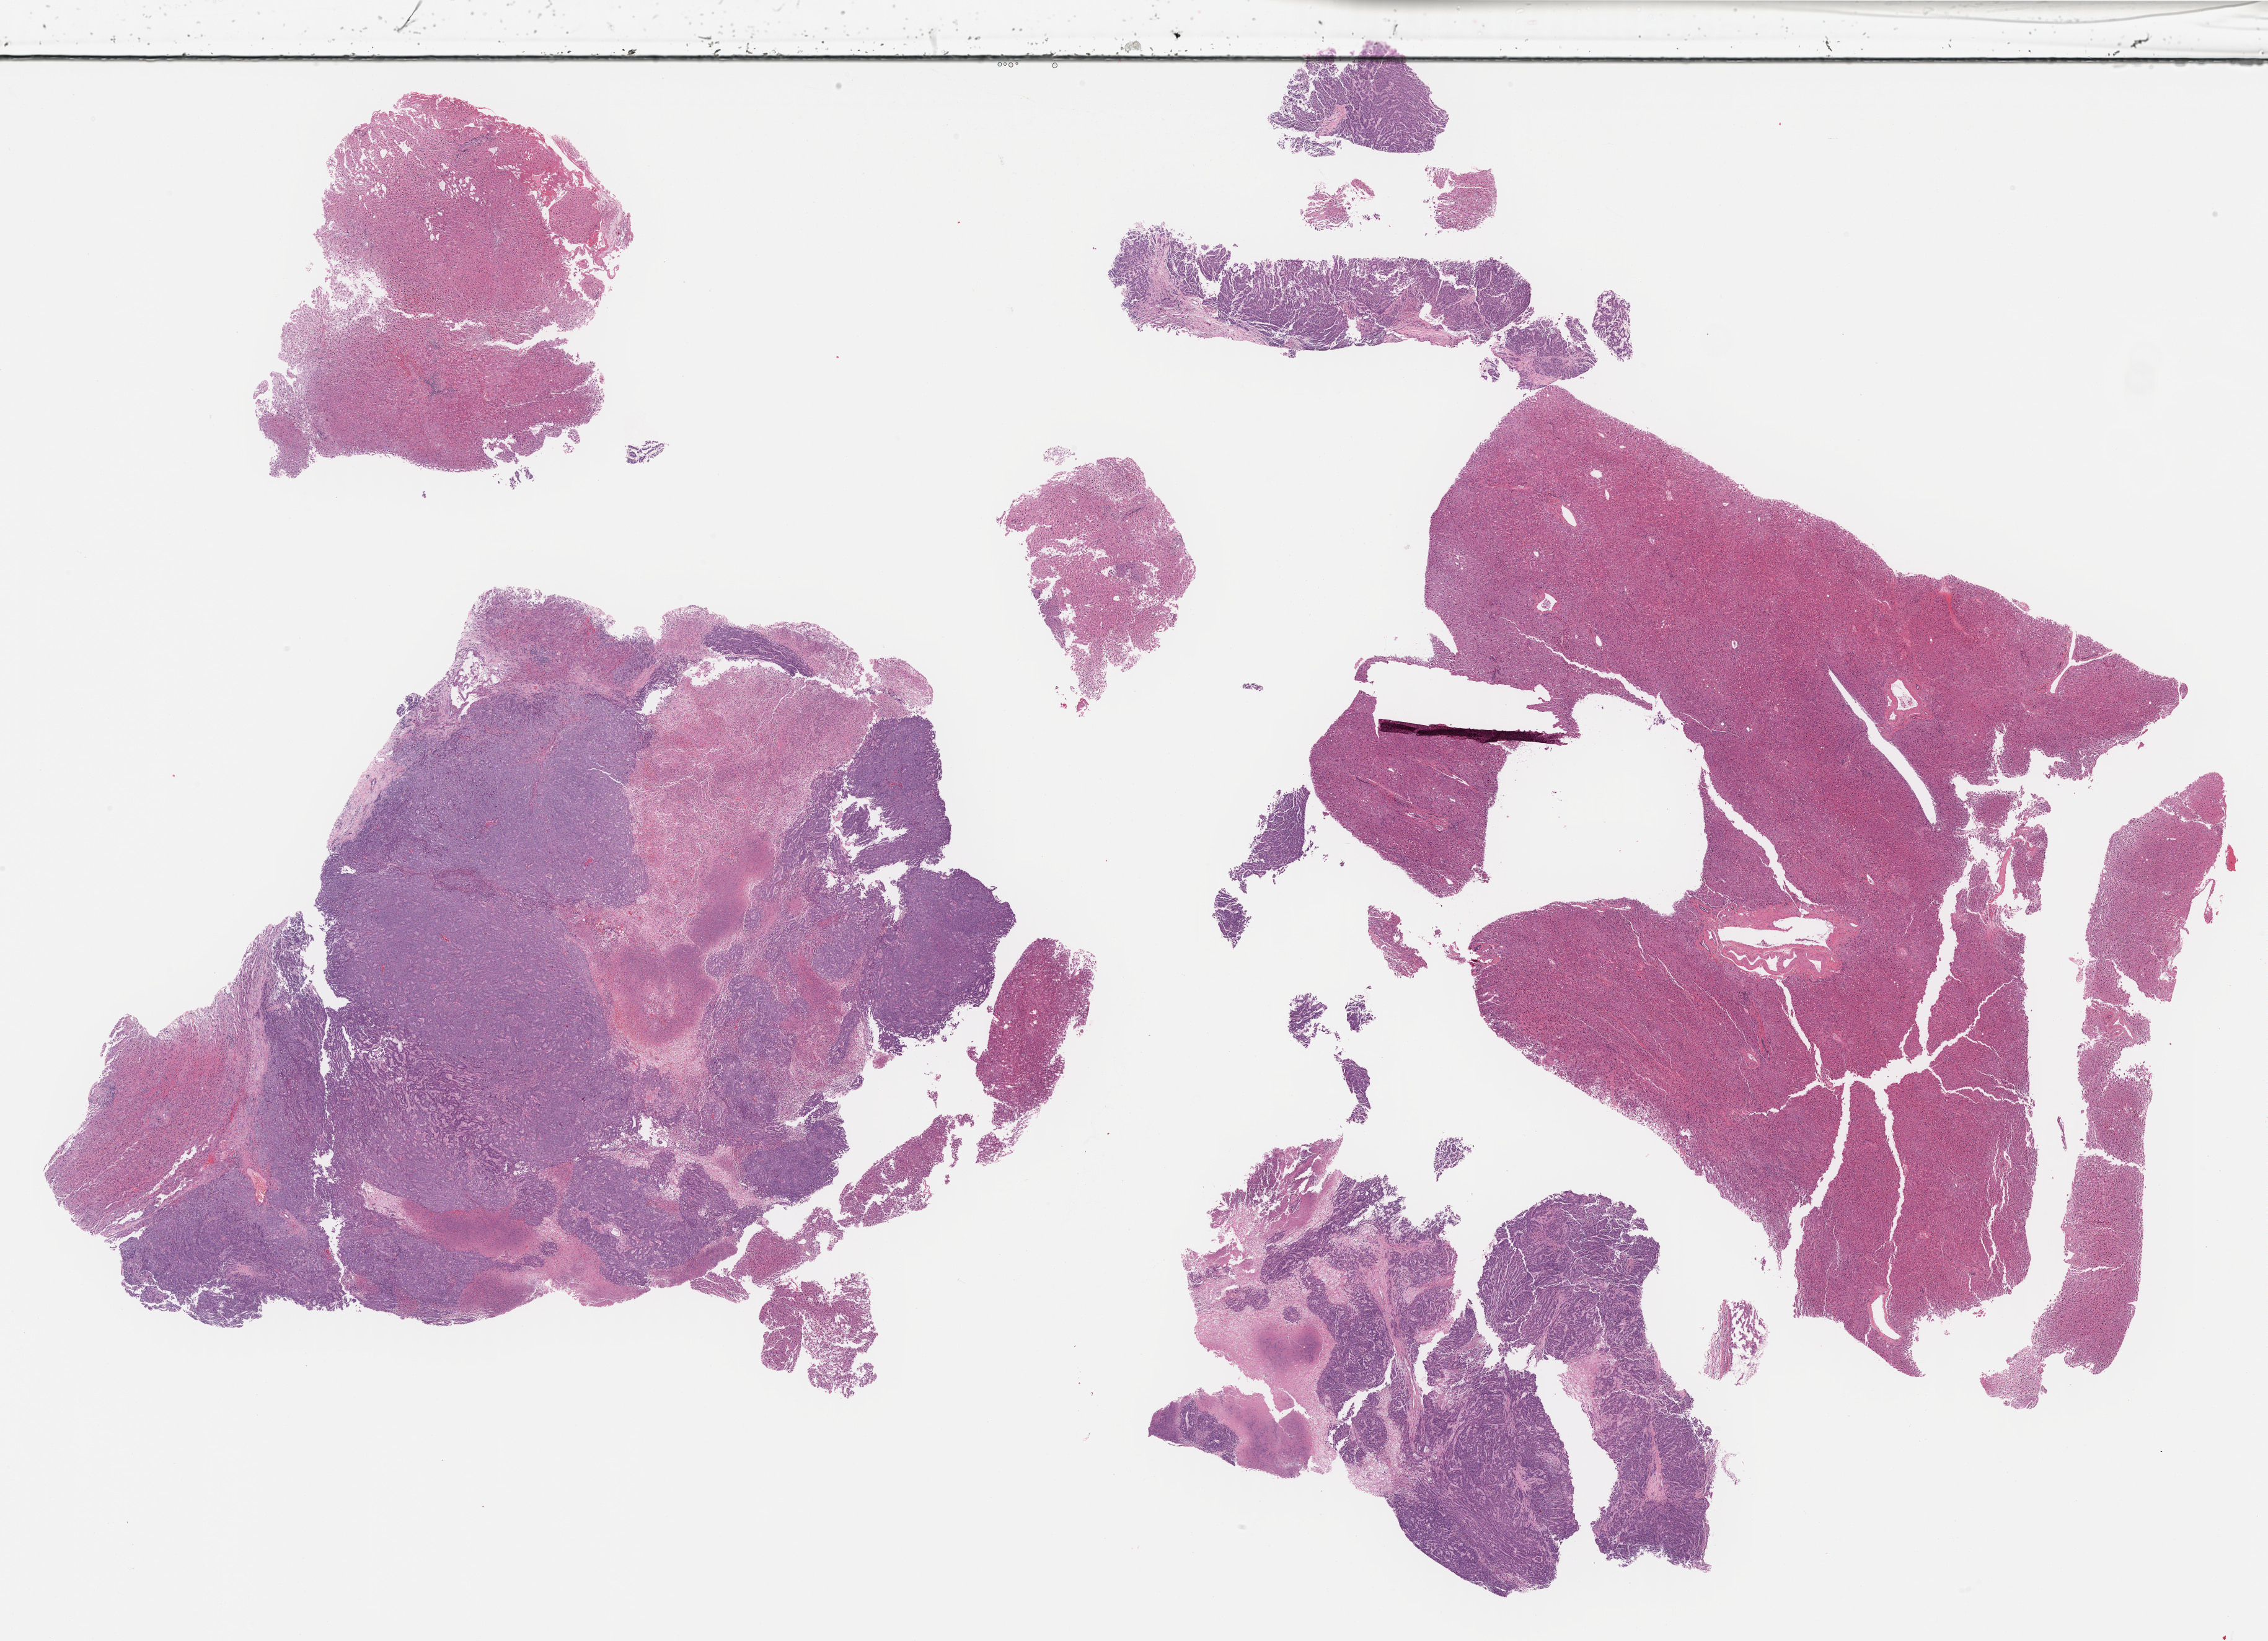
H&E whole-slide image — whole scanned area (about 29.6 x 21.4 mm) shown as a low-resolution overview, formalin-fixed paraffin-embedded (FFPE) diagnostic section, liver, primary tumour sample. Patient: female, age at initial diagnosis 81 years. Histologic grade: G4 (undifferentiated).
• AJCC pathologic stage: I
• histologic diagnosis: Combined hepatocellular carcinoma and cholangiocarcinoma